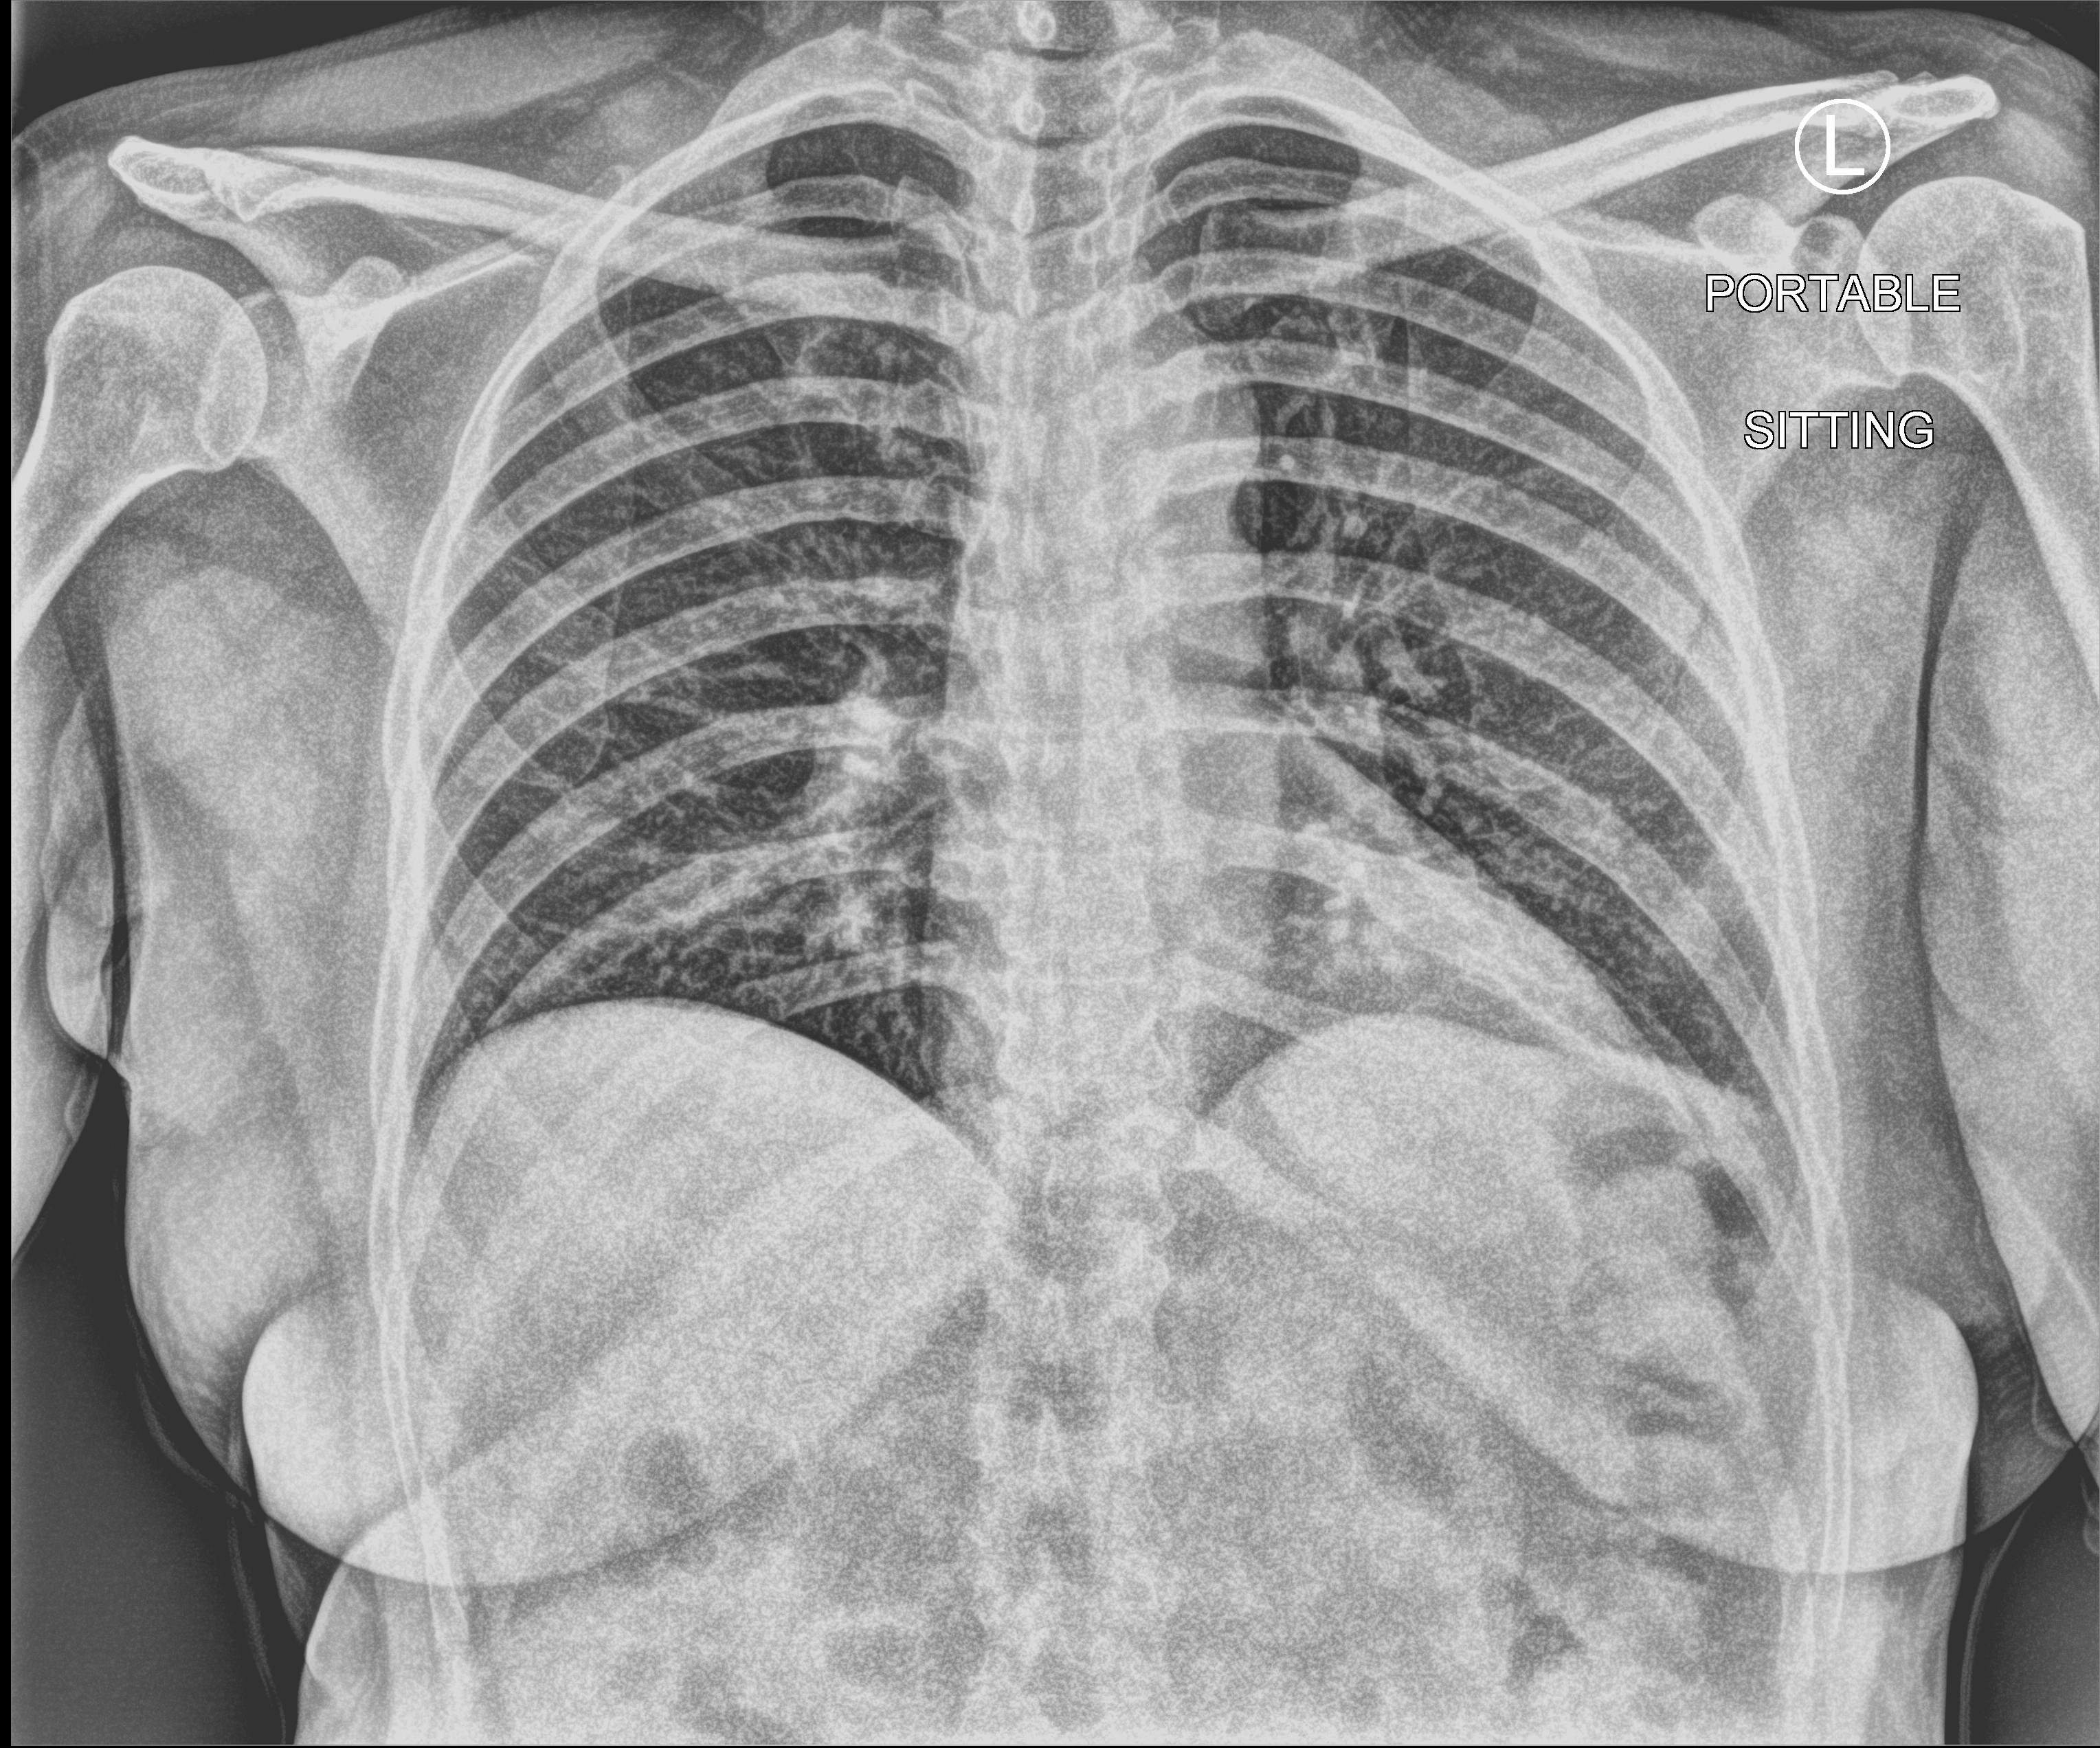
Bedside chest radiograph (computed radiography); anteroposterior (AP) projection. Patient hospitalised with COVID-19; female, aged 18–59 years.
Admission-level facts for this patient (not findings on this image; timing relative to this image not recorded): admitted to intensive care during this hospital stay: no.